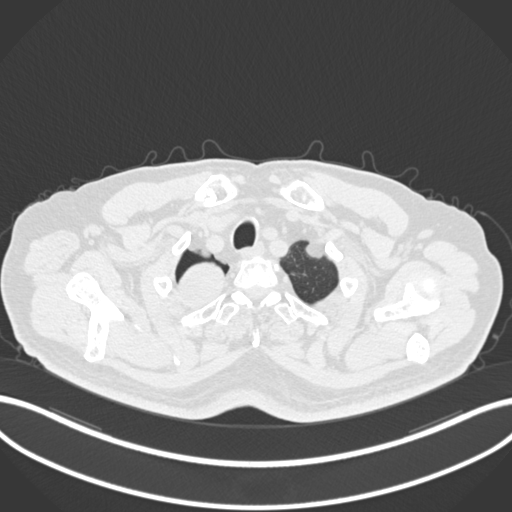
Chest CT, one axial slice; slice 198 of 218 in the series (ordered by position); reconstruction kernel B30f; 120 kVp; lung window (W 1500 / L -600 HU); 1 mm slice thickness; 512 × 512 image matrix, field of view 400 × 400 mm. Patient: male, 68 years. Case-level facts recorded for this patient, not image findings: clinical TNM (as recorded): T2a N0 M0.
Outlined on this slice (rectangle marked by the reading radiologist):
- lung tumour (recorded histology: adenocarcinoma): bounding box [x1, y1, x2, y2] px = [172, 259, 232, 310]